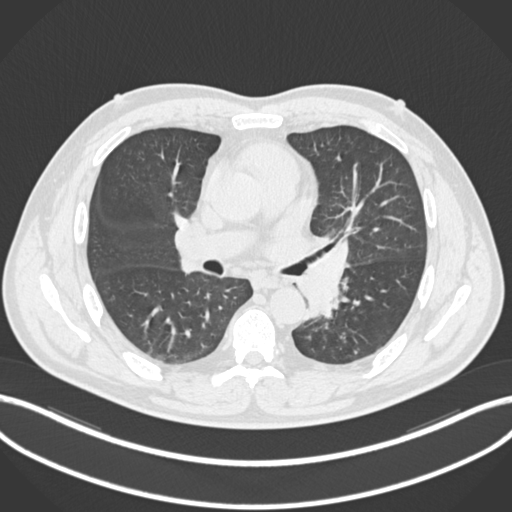
Chest CT, one axial slice. Position 126 of 223 along the scan axis. Lung window (W 1500 / L -600 HU). 512 × 512 image matrix, field of view 400 × 400 mm. Male patient, age 50 years. From the clinical record (not read from this slice): clinical TNM (as recorded): T2a N3 M0.
Structures marked on this image (rectangle marked by the reading radiologist):
- lung tumour (recorded histology: squamous cell carcinoma): box from (x=291, y=233) to (x=350, y=319) px